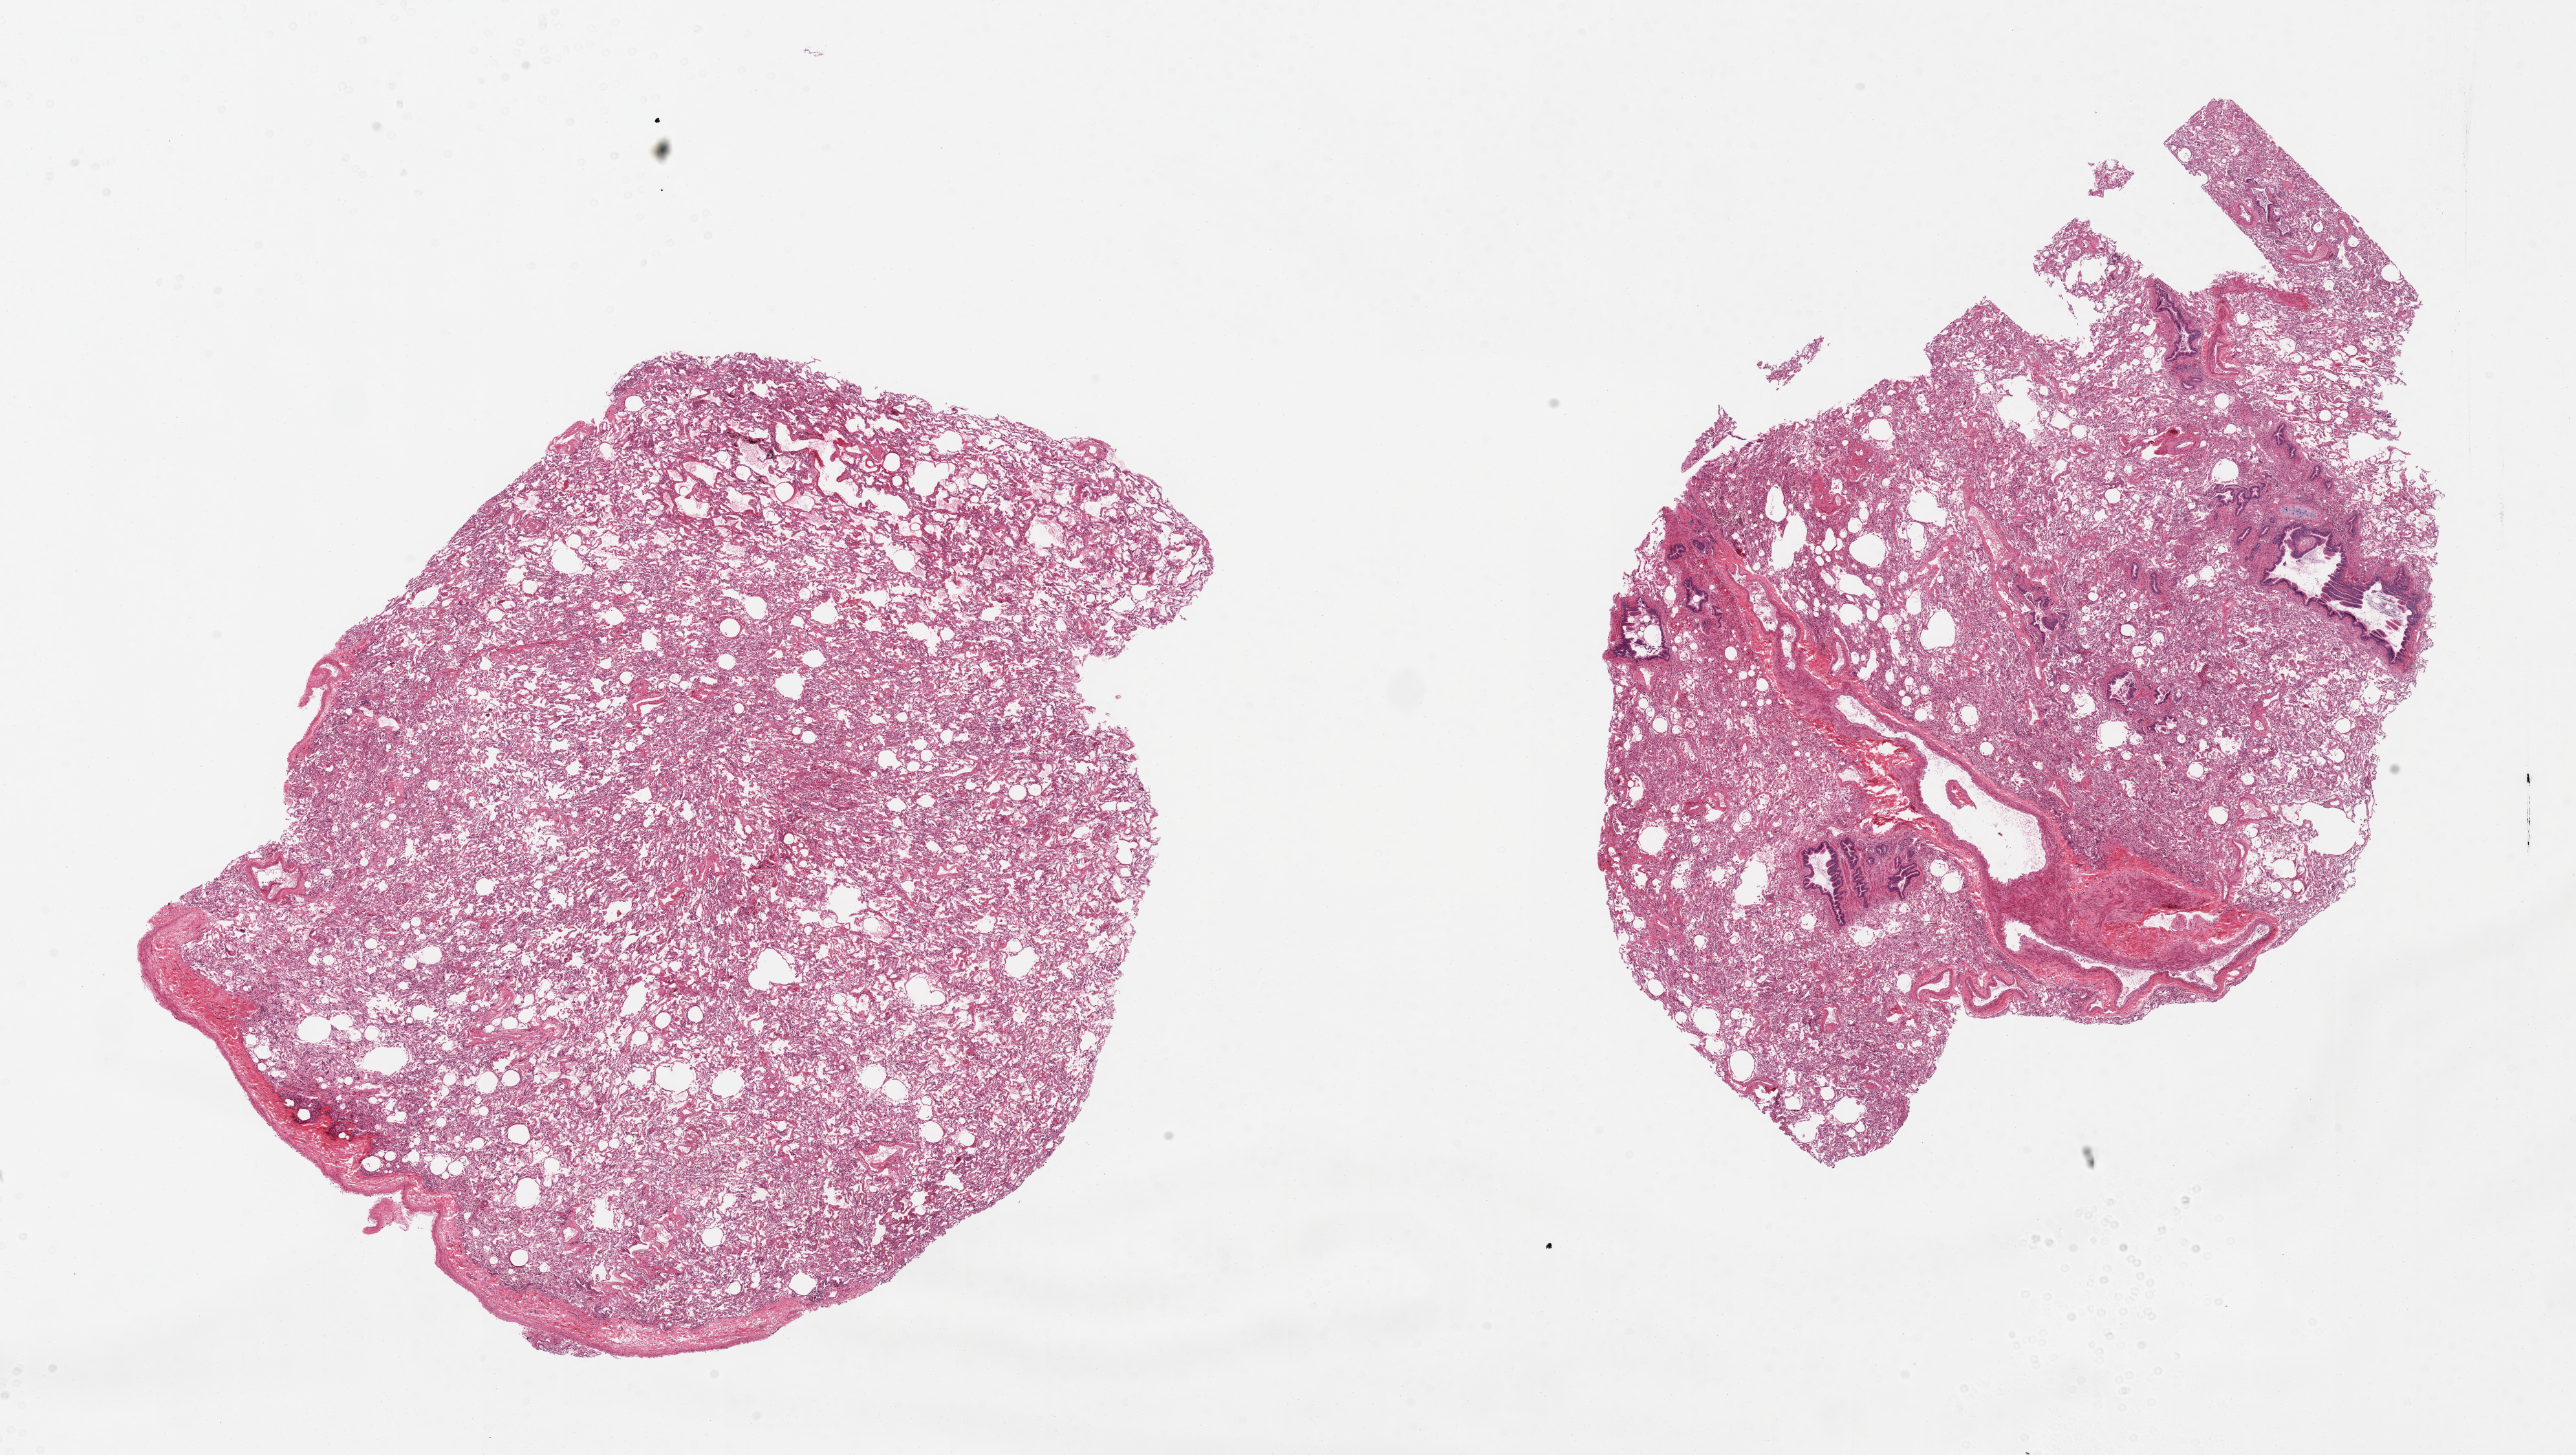
H&E whole-slide image, whole scanned area (about 31.5 x 17.8 mm) shown as a low-resolution overview. PAXgene-fixed, paraffin-embedded tissue. Section of lung (target tissue). Tissue donor sample. Donor: male.
Review note (as recorded): 2 pieces, numerous hemosiderin-laden macrophages, patchy bronchopneumonia, focus of cartilage.